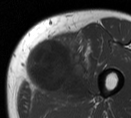
MRI of an extremity soft-tissue mass, one axial slice. Position 20 of 55 along the scan axis. MR volume resampled by the dataset authors to the PET/CT grid (not the native acquisition matrix). 3.27 mm slice thickness. 131 × 118 image matrix, field of view 128 × 115 mm. Male patient. From the clinical record (not read from this slice): histological type: pleiomorphic liposarcoma; grade: high; site of the primary tumour: left thigh.
Outlined on this slice (expert contour drawn on MRI and transferred to this co-registered scan by the dataset authors):
- gross tumour volume including surrounding oedema: bounding box <25,34,95,102> (left, top, right, bottom; pixels)
- gross tumour volume (mass): <25,36,88,95>